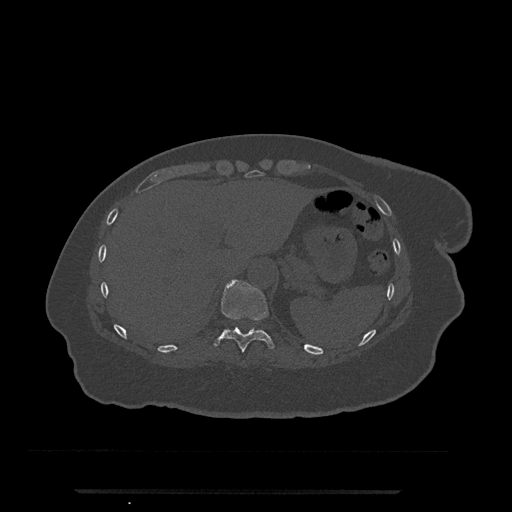
CT including the spine, one axial slice; reconstruction kernel Br40s/3; 120 kVp; bone window (W 1800 / L 400 HU); 0.5 mm slice thickness; 512 × 512 image matrix. Patient: female, 51 years. From the clinical record (not read from this slice): primary cancer: neuro.
Outlined on this slice (semi-automatically segmented with operator editing):
- T10 vertebra: bounding box [x1, y1, x2, y2] px = [213, 279, 275, 352]